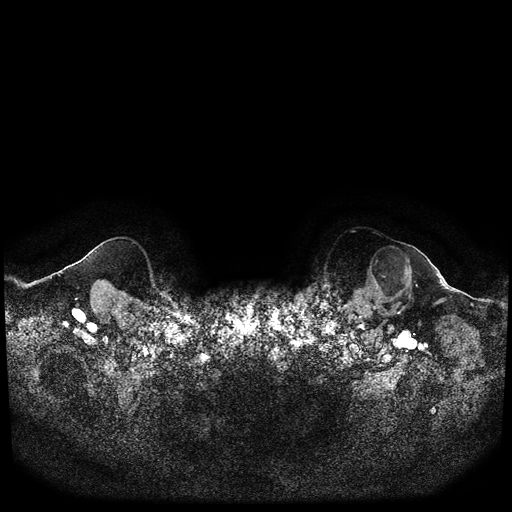
Breast MRI (dynamic contrast-enhanced, multi-phase), one axial slice. Position 102 of 116 along the scan axis. Dynamic contrast-enhanced series, time point 2 of 5 at this slice position (early post-contrast). 1.5 T. TE 2.6 ms, TR 5.3 ms. 2 mm slice thickness. 512 × 512 image matrix, field of view 350 × 350 mm. Female patient, age 64 years.
Annotated regions visible in this slice (semi-automatic segmentation, software-assisted and operator-edited):
- breast lesion (labelled 'tumour' in the annotation; benign lesions carry a separate 'benign' label): box from (x=367, y=244) to (x=413, y=304) px